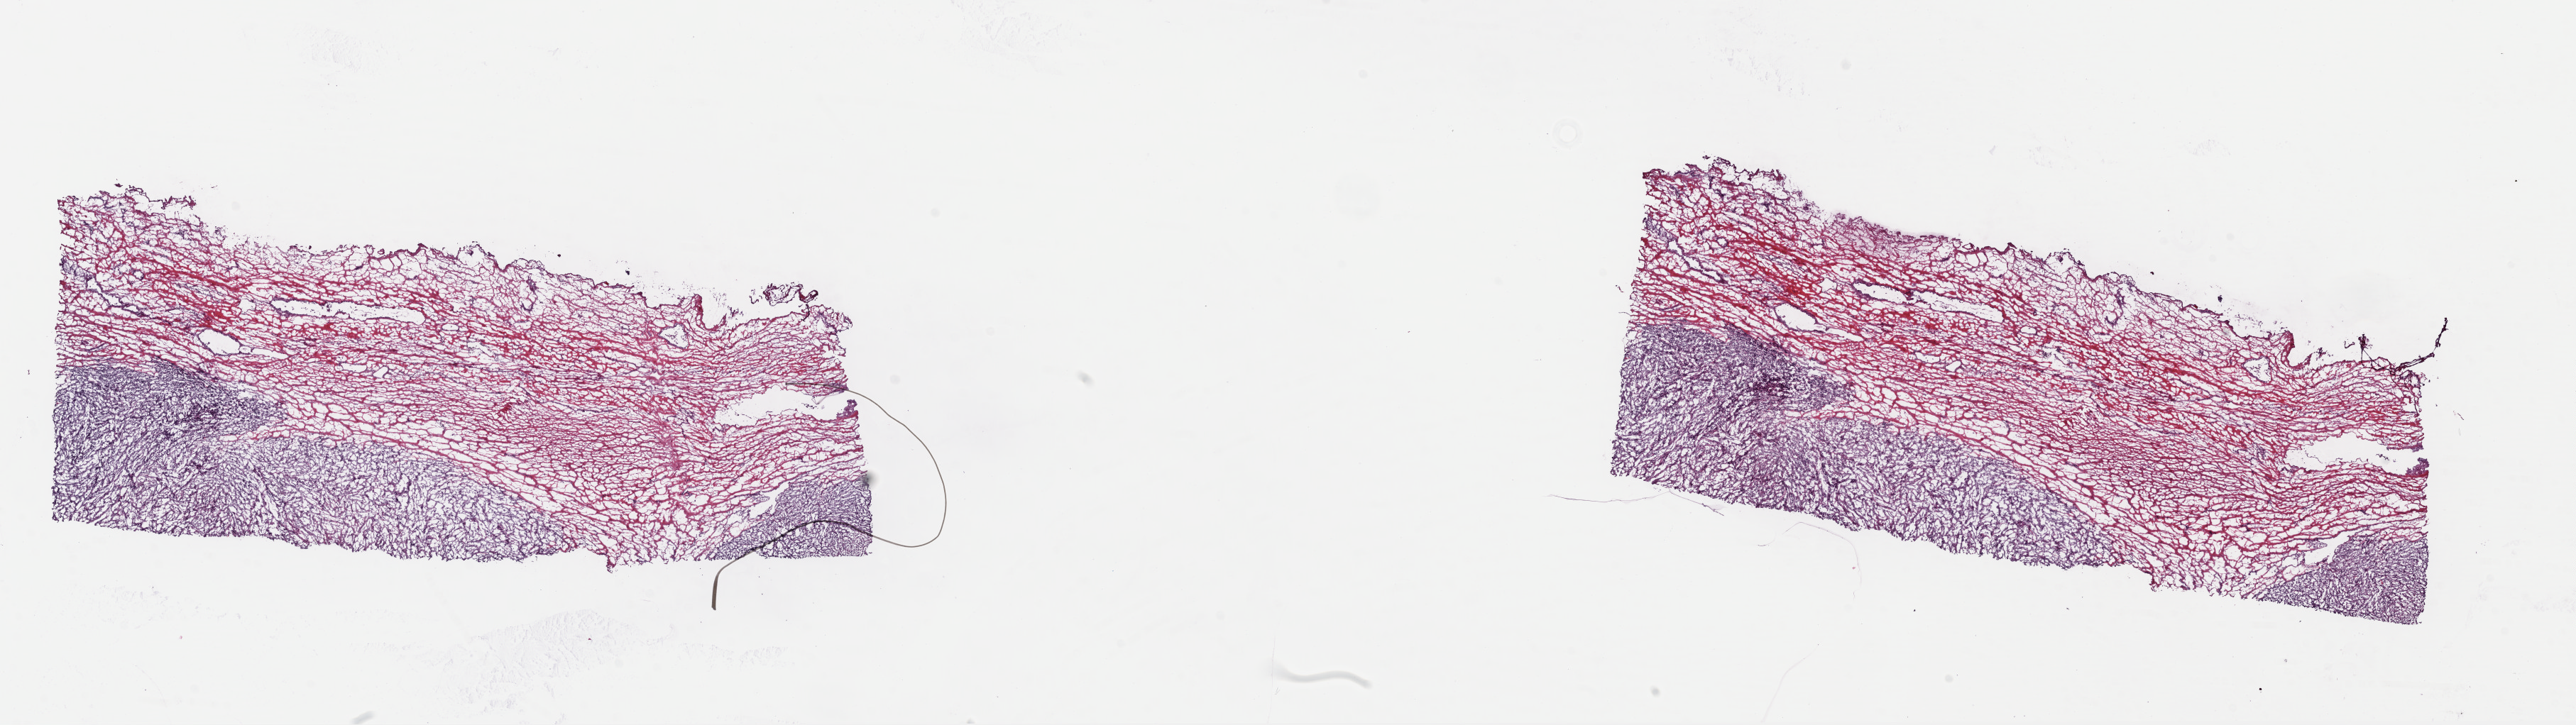
Whole-slide histology image, Hematoxylin and eosin (H&E) stained — a low-resolution overview of the entire scanned area, about 28.5 x 8.0 mm (acquisition: 40x scan); frozen section from the top of the tissue portion; retroperitoneum and peritoneum, primary tumour sample. Female, age 77 years at initial diagnosis.
Pathologic diagnosis: Leiomyosarcoma, NOS.